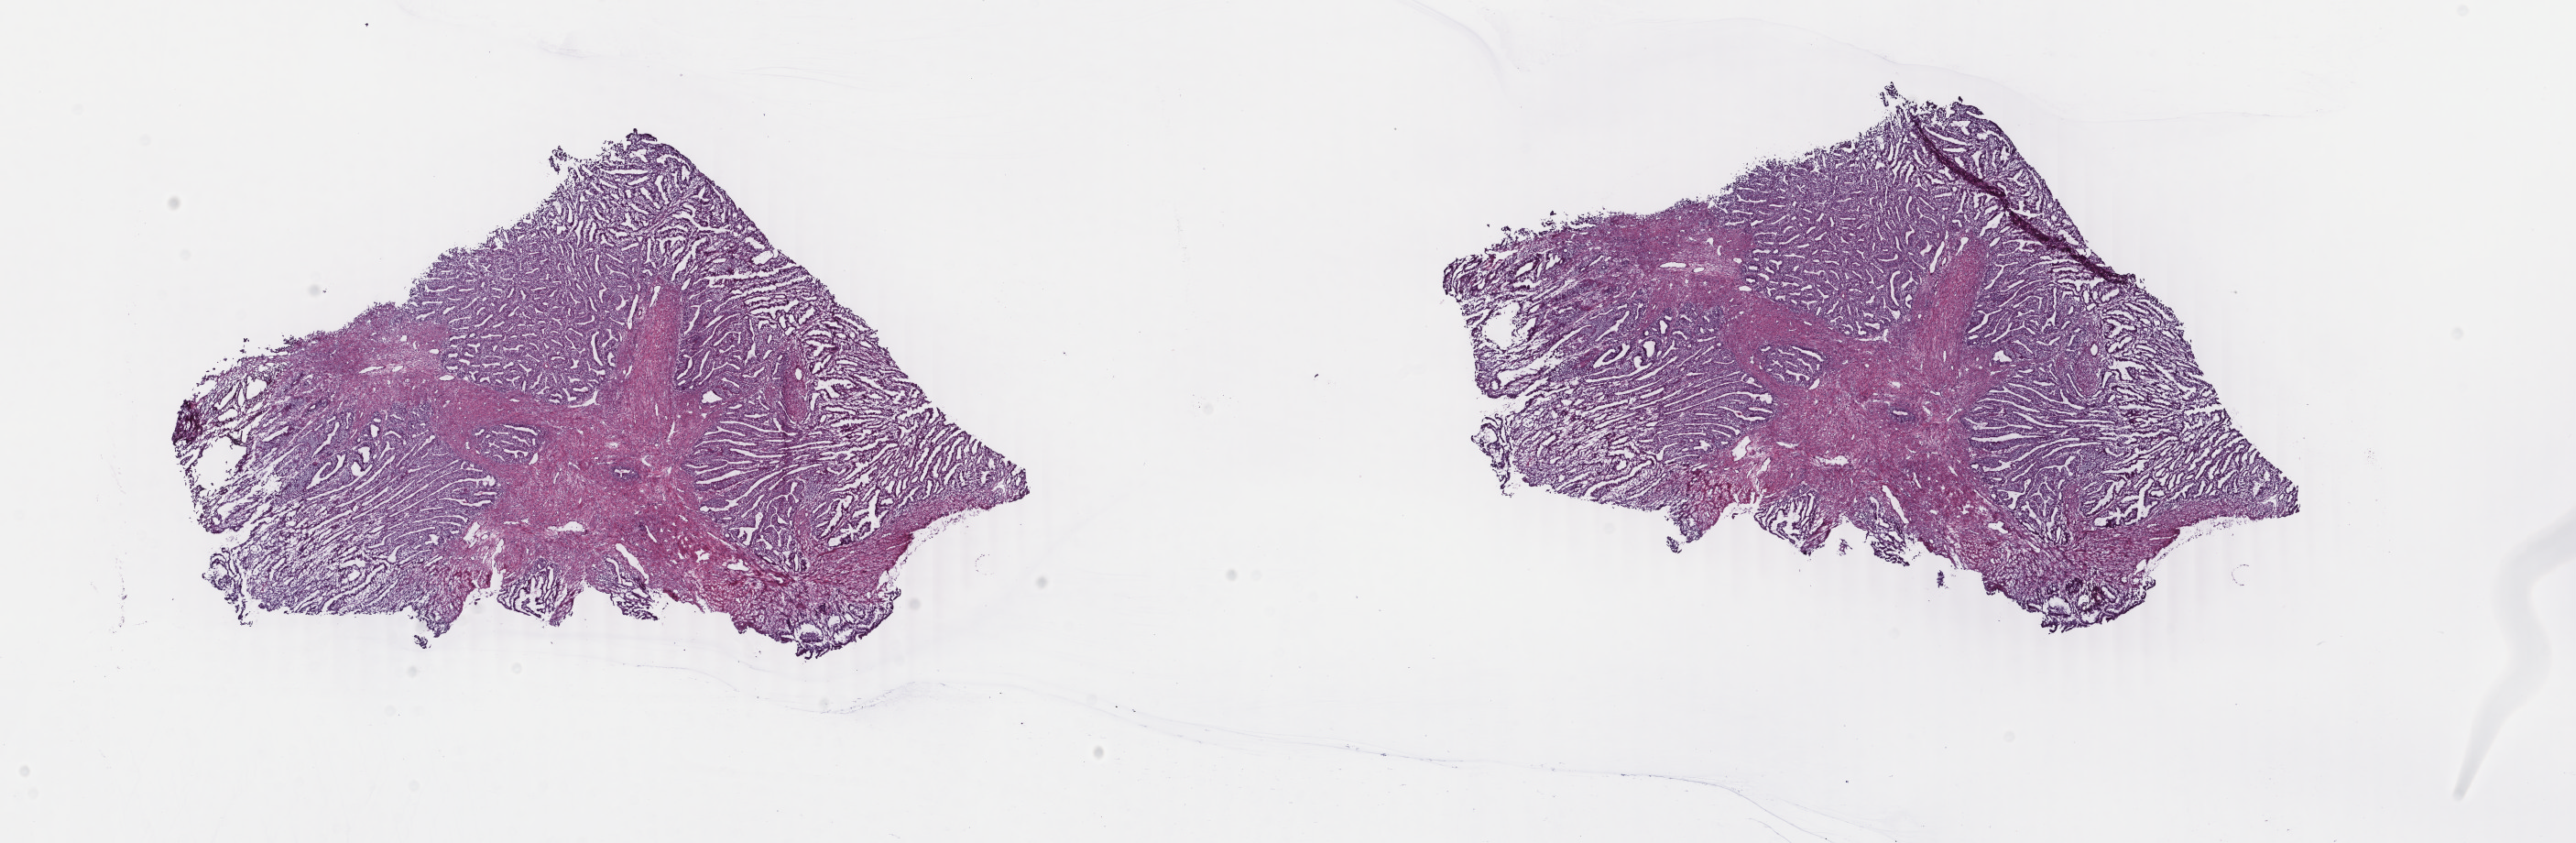
Whole-slide histology image, H&E, low-resolution overview of the scanned area, about 22.4 x 7.3 mm (acquisition: 40x scan); frozen section from the top of the tissue portion; uterus, primary tumour sample. Patient: female, age at initial diagnosis 61 years. Histologic grade: G1 (well differentiated). Composition of this section per pathologist review: tumour cells 60%, tumour nuclei 60%, normal cells 0%, stromal cells 40%, necrosis 0%. Inflammatory infiltration, as recorded: lymphocyte infiltration 5%, monocyte infiltration 0%, neutrophil infiltration 0%.
Histologic diagnosis: Endometrioid adenocarcinoma, NOS (endometrium). FIGO stage: IB. Lymph nodes positive (case pathology): 0 of 28 examined.